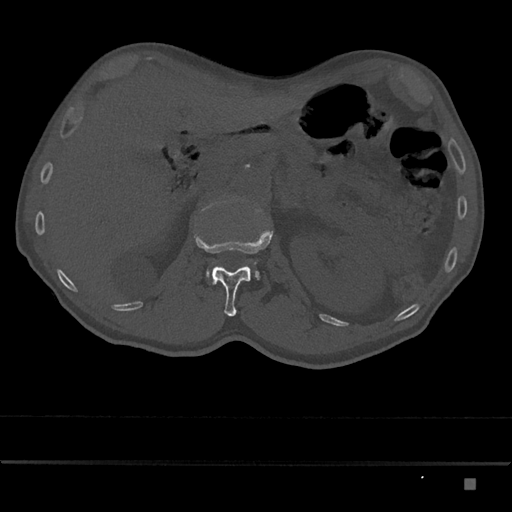
CT including the spine, one axial slice; slice 528 of 797 in the series (ordered by position); reconstruction kernel Br40s/3; bone window (W 1800 / L 400 HU); 0.5 mm slice thickness; 512 × 512 image matrix, field of view 390 × 390 mm. Patient: male, 72 years. From the clinical record (not read from this slice): primary cancer: prostate.
Outlined on this slice (semi-automatic segmentation, software-assisted and operator-edited):
- L1 vertebra: bounding box <194,230,273,317> (left, top, right, bottom; pixels)
- L2 vertebra: <206,262,261,280>